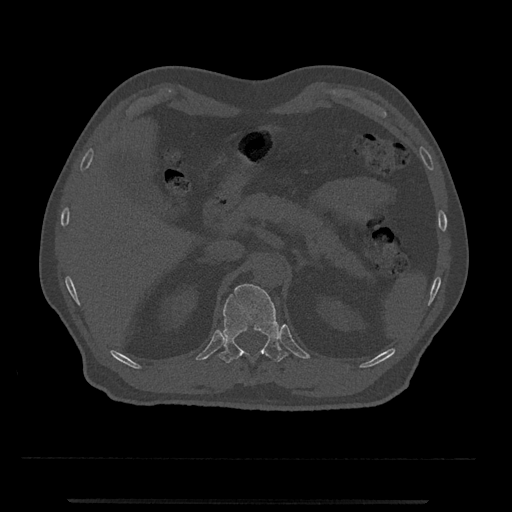
CT including the spine, one axial slice; position 410 of 797 along the scan axis; reconstruction kernel Br40s/3; 120 kVp; bone window (W 1800 / L 400 HU); 0.5 mm slice thickness; 512 × 512 image matrix, field of view 419 × 419 mm. Male patient, age 63 years. From the clinical record (not read from this slice): primary cancer: prostate.
Outlined on this slice (semi-automatic segmentation, software-assisted and operator-edited):
- T12 vertebra: bounding box (x1, y1, x2, y2) in pixels: (218, 284, 288, 363)